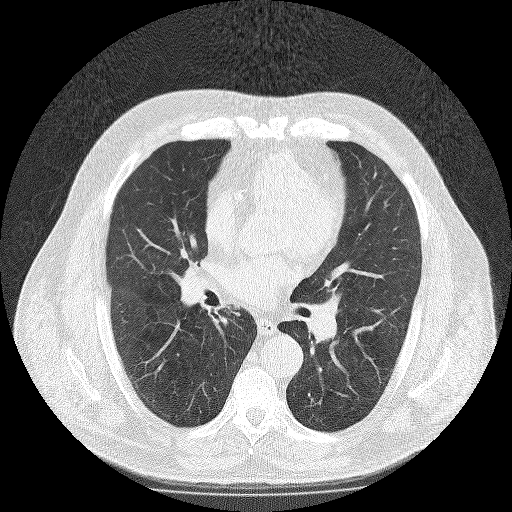
Axial slice from a low-dose chest CT screening exam. Second screening round (one year after baseline). Lung window (W 1500 / L -600 HU). 2 mm slice thickness. Lung (sharp) reconstruction kernel (FC51). 120 kVp. Slice 86 of 188 in the series. Male, age 65 years at enrolment. Former smoker at enrolment.
- Expert-annotated lung lesion, box from (x=203, y=295) to (x=249, y=331) px.
- Screening reader's record for this exam (one nodule recorded; not confirmed to be the boxed lesion): non-calcified nodule or mass ≥4 mm, right lower lobe, 10 × 9 mm, spiculated (stellate) margins, soft tissue attenuation, pre-existing on the prior screen: yes; interval growth: no.